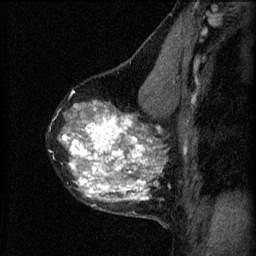
Breast MRI (dynamic contrast-enhanced), one sagittal slice; position 39 of 60 along the scan axis; 3 images stored at this slice position (order not interpretable as contrast timing); 1.5 T; TE 4.2 ms, TR 8.2 ms; 2 mm slice thickness; 256 × 256 image matrix, field of view 180 × 180 mm. Patient: female, 40 years.
Annotated regions visible in this slice (semi-automatically segmented with operator editing):
- analysis volume of interest (the breast-tissue region the enhancement analysis was run in; not a lesion): bounding box (x1, y1, x2, y2) in pixels: (48, 76, 179, 219)
- tumour enhancement mask (voxels above the 70 % enhancement threshold inside the analysis volume of interest): (62, 100, 163, 201)